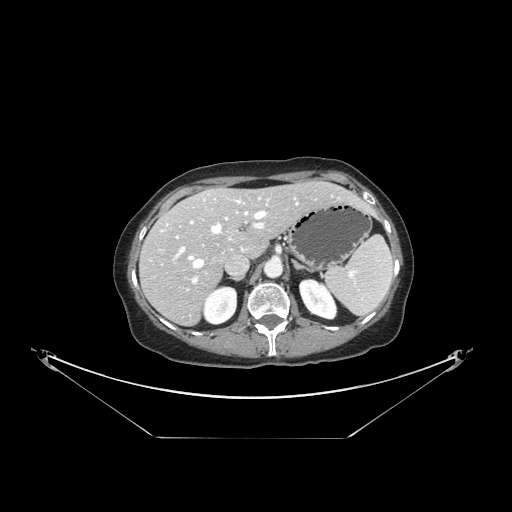
Contrast-enhanced abdominal CT, one axial slice; position 98 of 148 along the scan axis; reconstruction kernel STANDARD; soft-tissue window (W 400 / L 40 HU); 2.5 mm slice thickness; 512 × 512 image matrix. Female patient, age 73 years. Case-level facts recorded for this patient, not image findings: diagnosis: colorectal cancer liver metastases, imaged before liver resection; multiple liver metastases: no; largest metastasis: 1 cm; chemotherapy before resection: yes.
Structures marked on this image (expert manual segmentation):
- hepatic veins: bounding box (x1, y1, x2, y2) in pixels: (189, 198, 298, 268)
- liver: (141, 182, 364, 325)
- planned liver remnant (the part of the liver to remain after resection): (168, 182, 363, 256)
- portal vein (with intrahepatic branches): (175, 204, 268, 284)